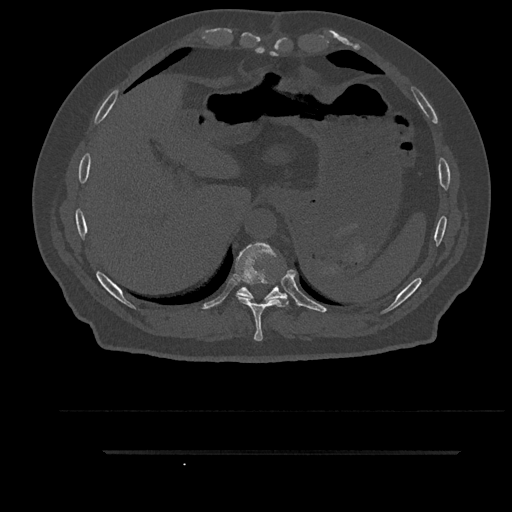
CT including the spine, one axial slice; 120 kVp; bone window (W 1800 / L 400 HU); 0.5 mm slice thickness; 512 × 512 image matrix, field of view 432 × 432 mm. Male patient, age 63 years. From the clinical record (not read from this slice): primary cancer: renal; vertebrae with lytic lesions (as recorded): T8.
Structures marked on this image (semi-automatic segmentation, software-assisted and operator-edited):
- T10 vertebra: bounding box (x1, y1, x2, y2) in pixels: (236, 286, 288, 301)
- T9 vertebra: (235, 243, 289, 341)